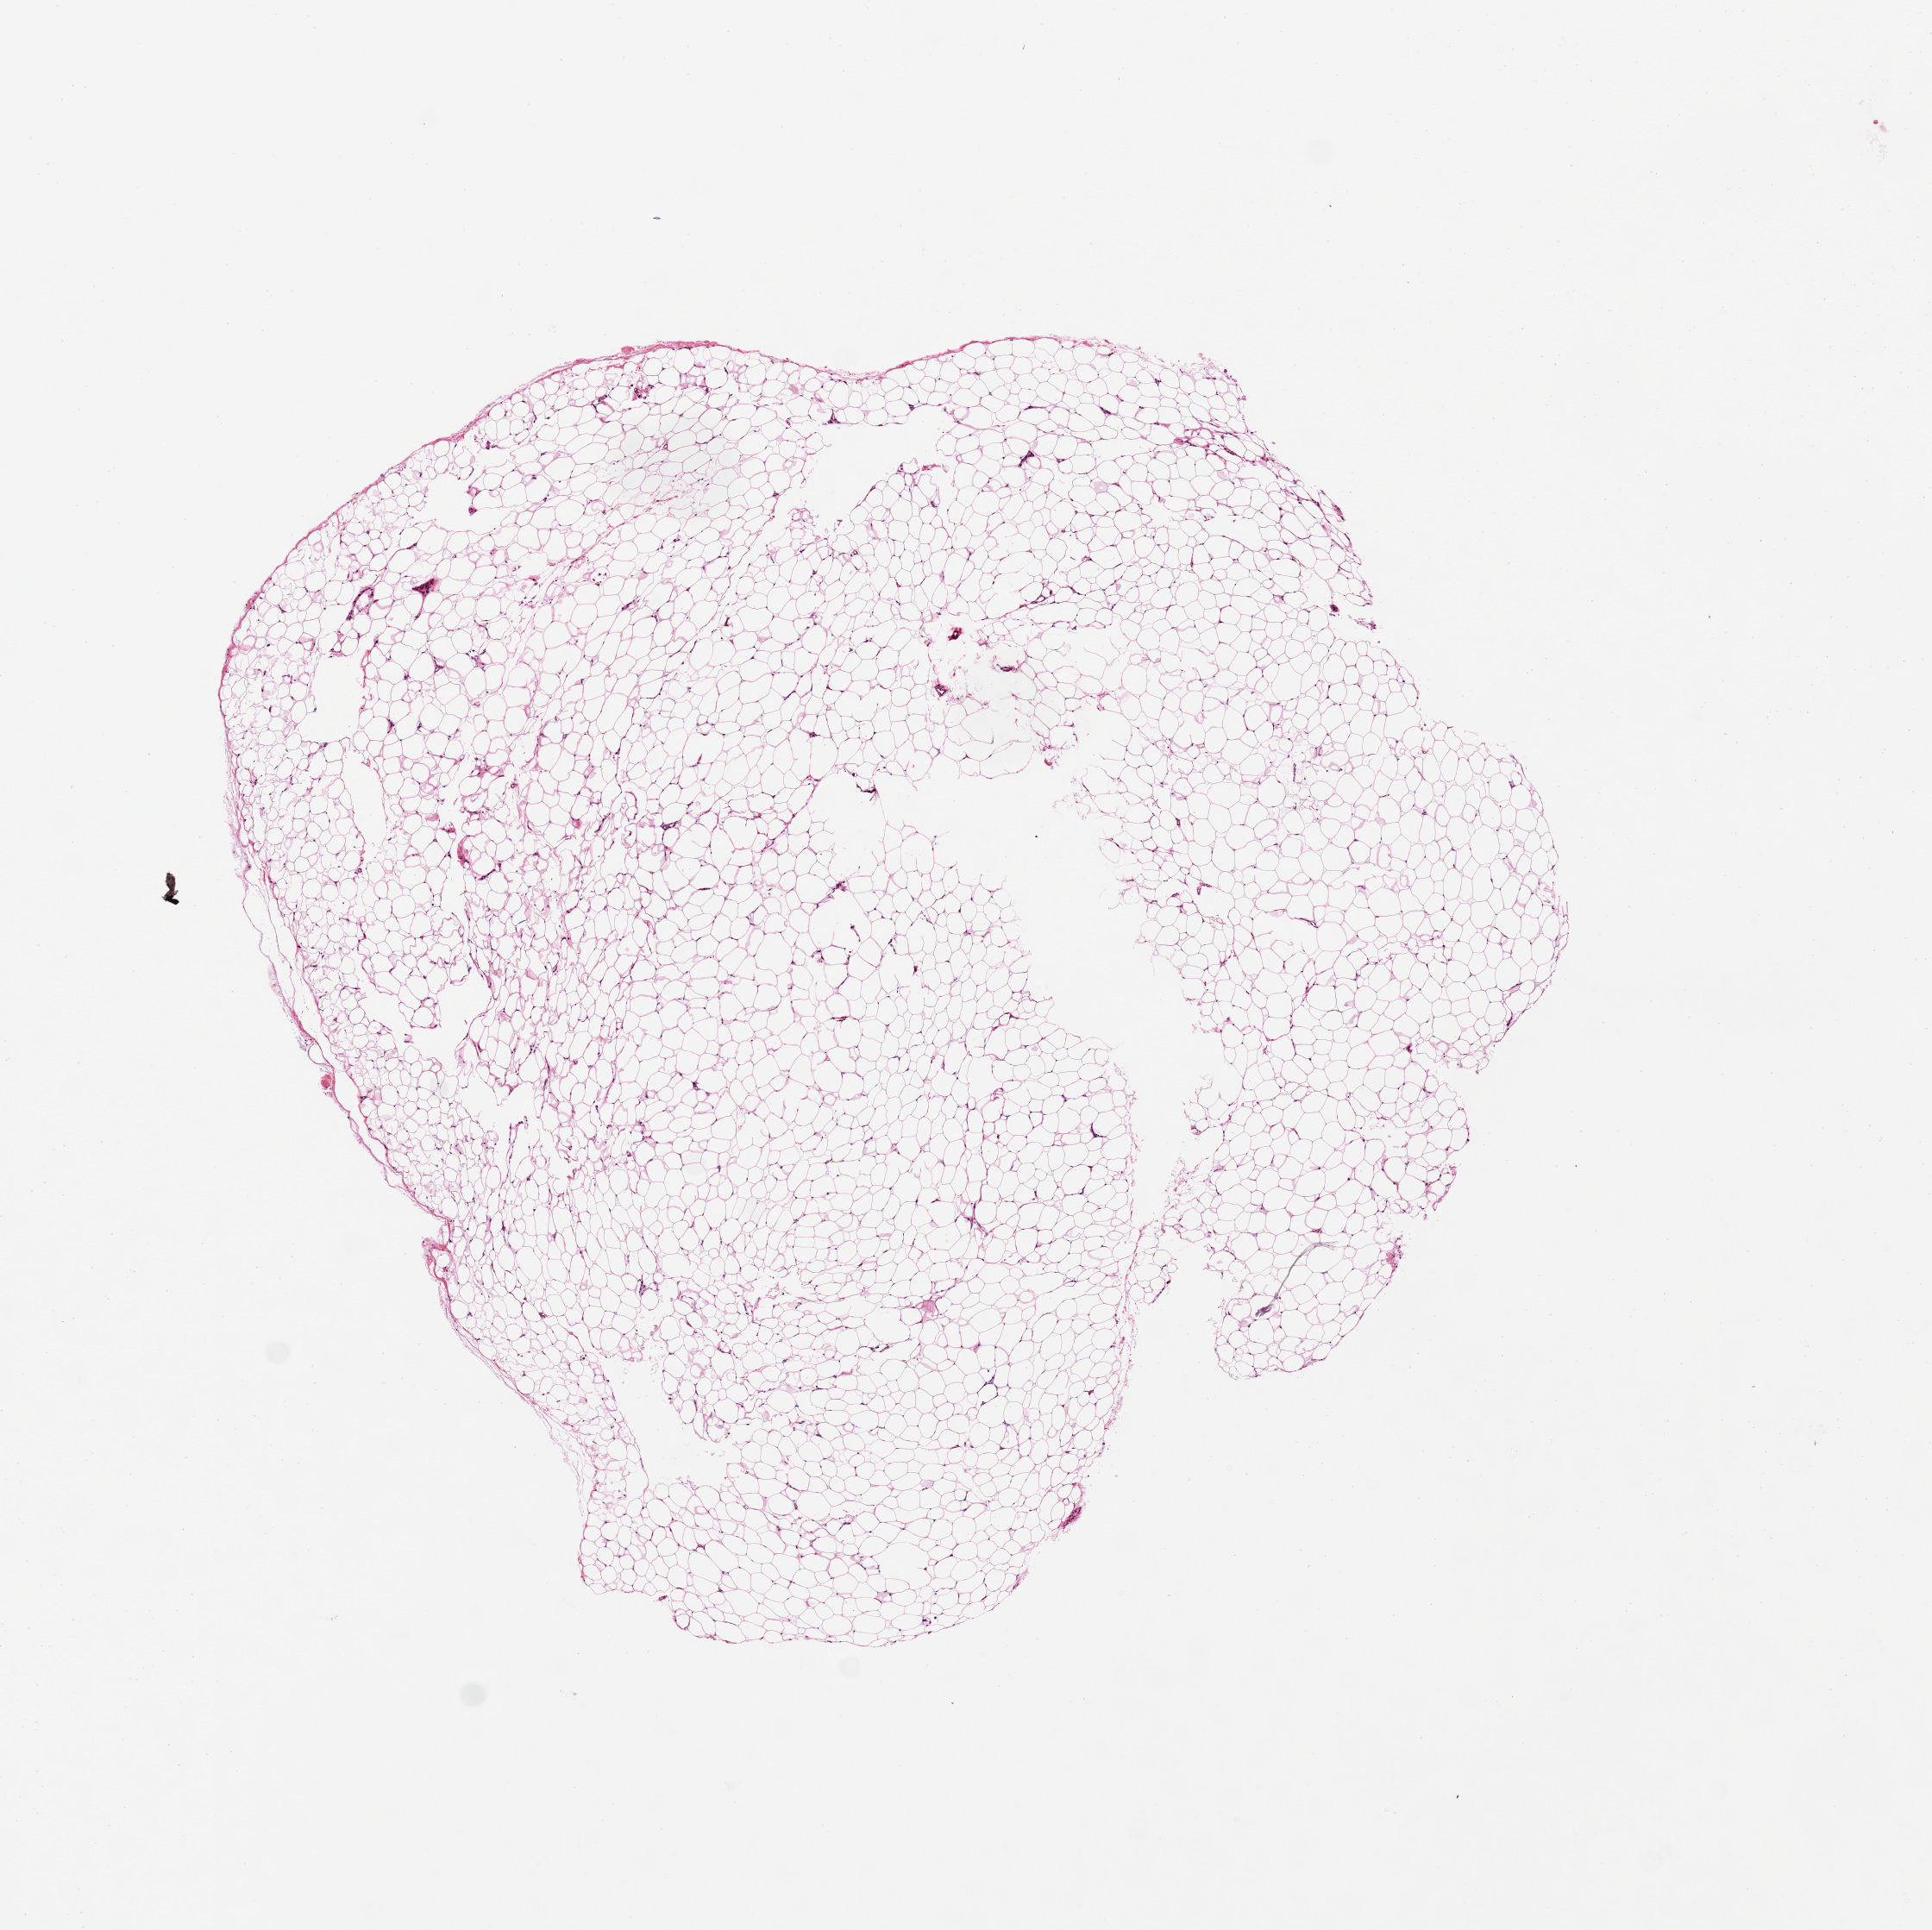
Digitized haematoxylin and eosin-stained section — shown as a low-resolution overview of the whole scanned area (about 8.9 x 8.9 mm, slide scanned at 20x). PAXgene-fixed paraffin-embedded (PFPE) section. Sampled site (target tissue): adipose tissue. Donor tissue sample. Donor sex: male.
• review note (as recorded): 1. 5.7x5.4mm. Small central area (~15-20%)poorly fixed